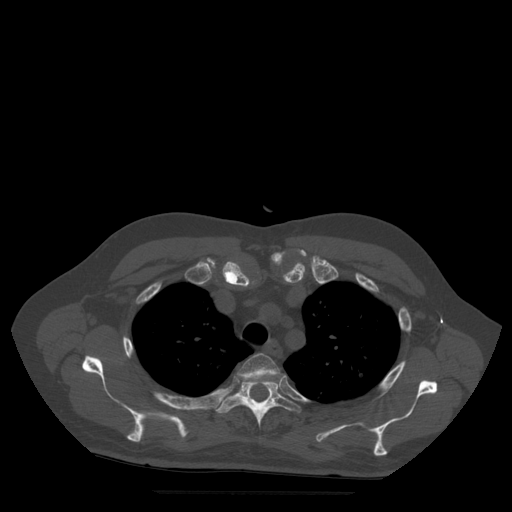
CT including the spine, one axial slice. Slice 397 of 522 in the series (ordered by position). Bone window (W 1800 / L 400 HU). 1.25 mm slice thickness. 512 × 512 image matrix. Patient age 72 years. From the clinical record (not read from this slice): primary cancer: prostate.
Structures marked on this image (semi-automatically segmented with operator editing):
- T3 vertebra: bounding box (x1, y1, x2, y2) in pixels: (238, 354, 280, 384)
- T4 vertebra: (216, 378, 302, 427)